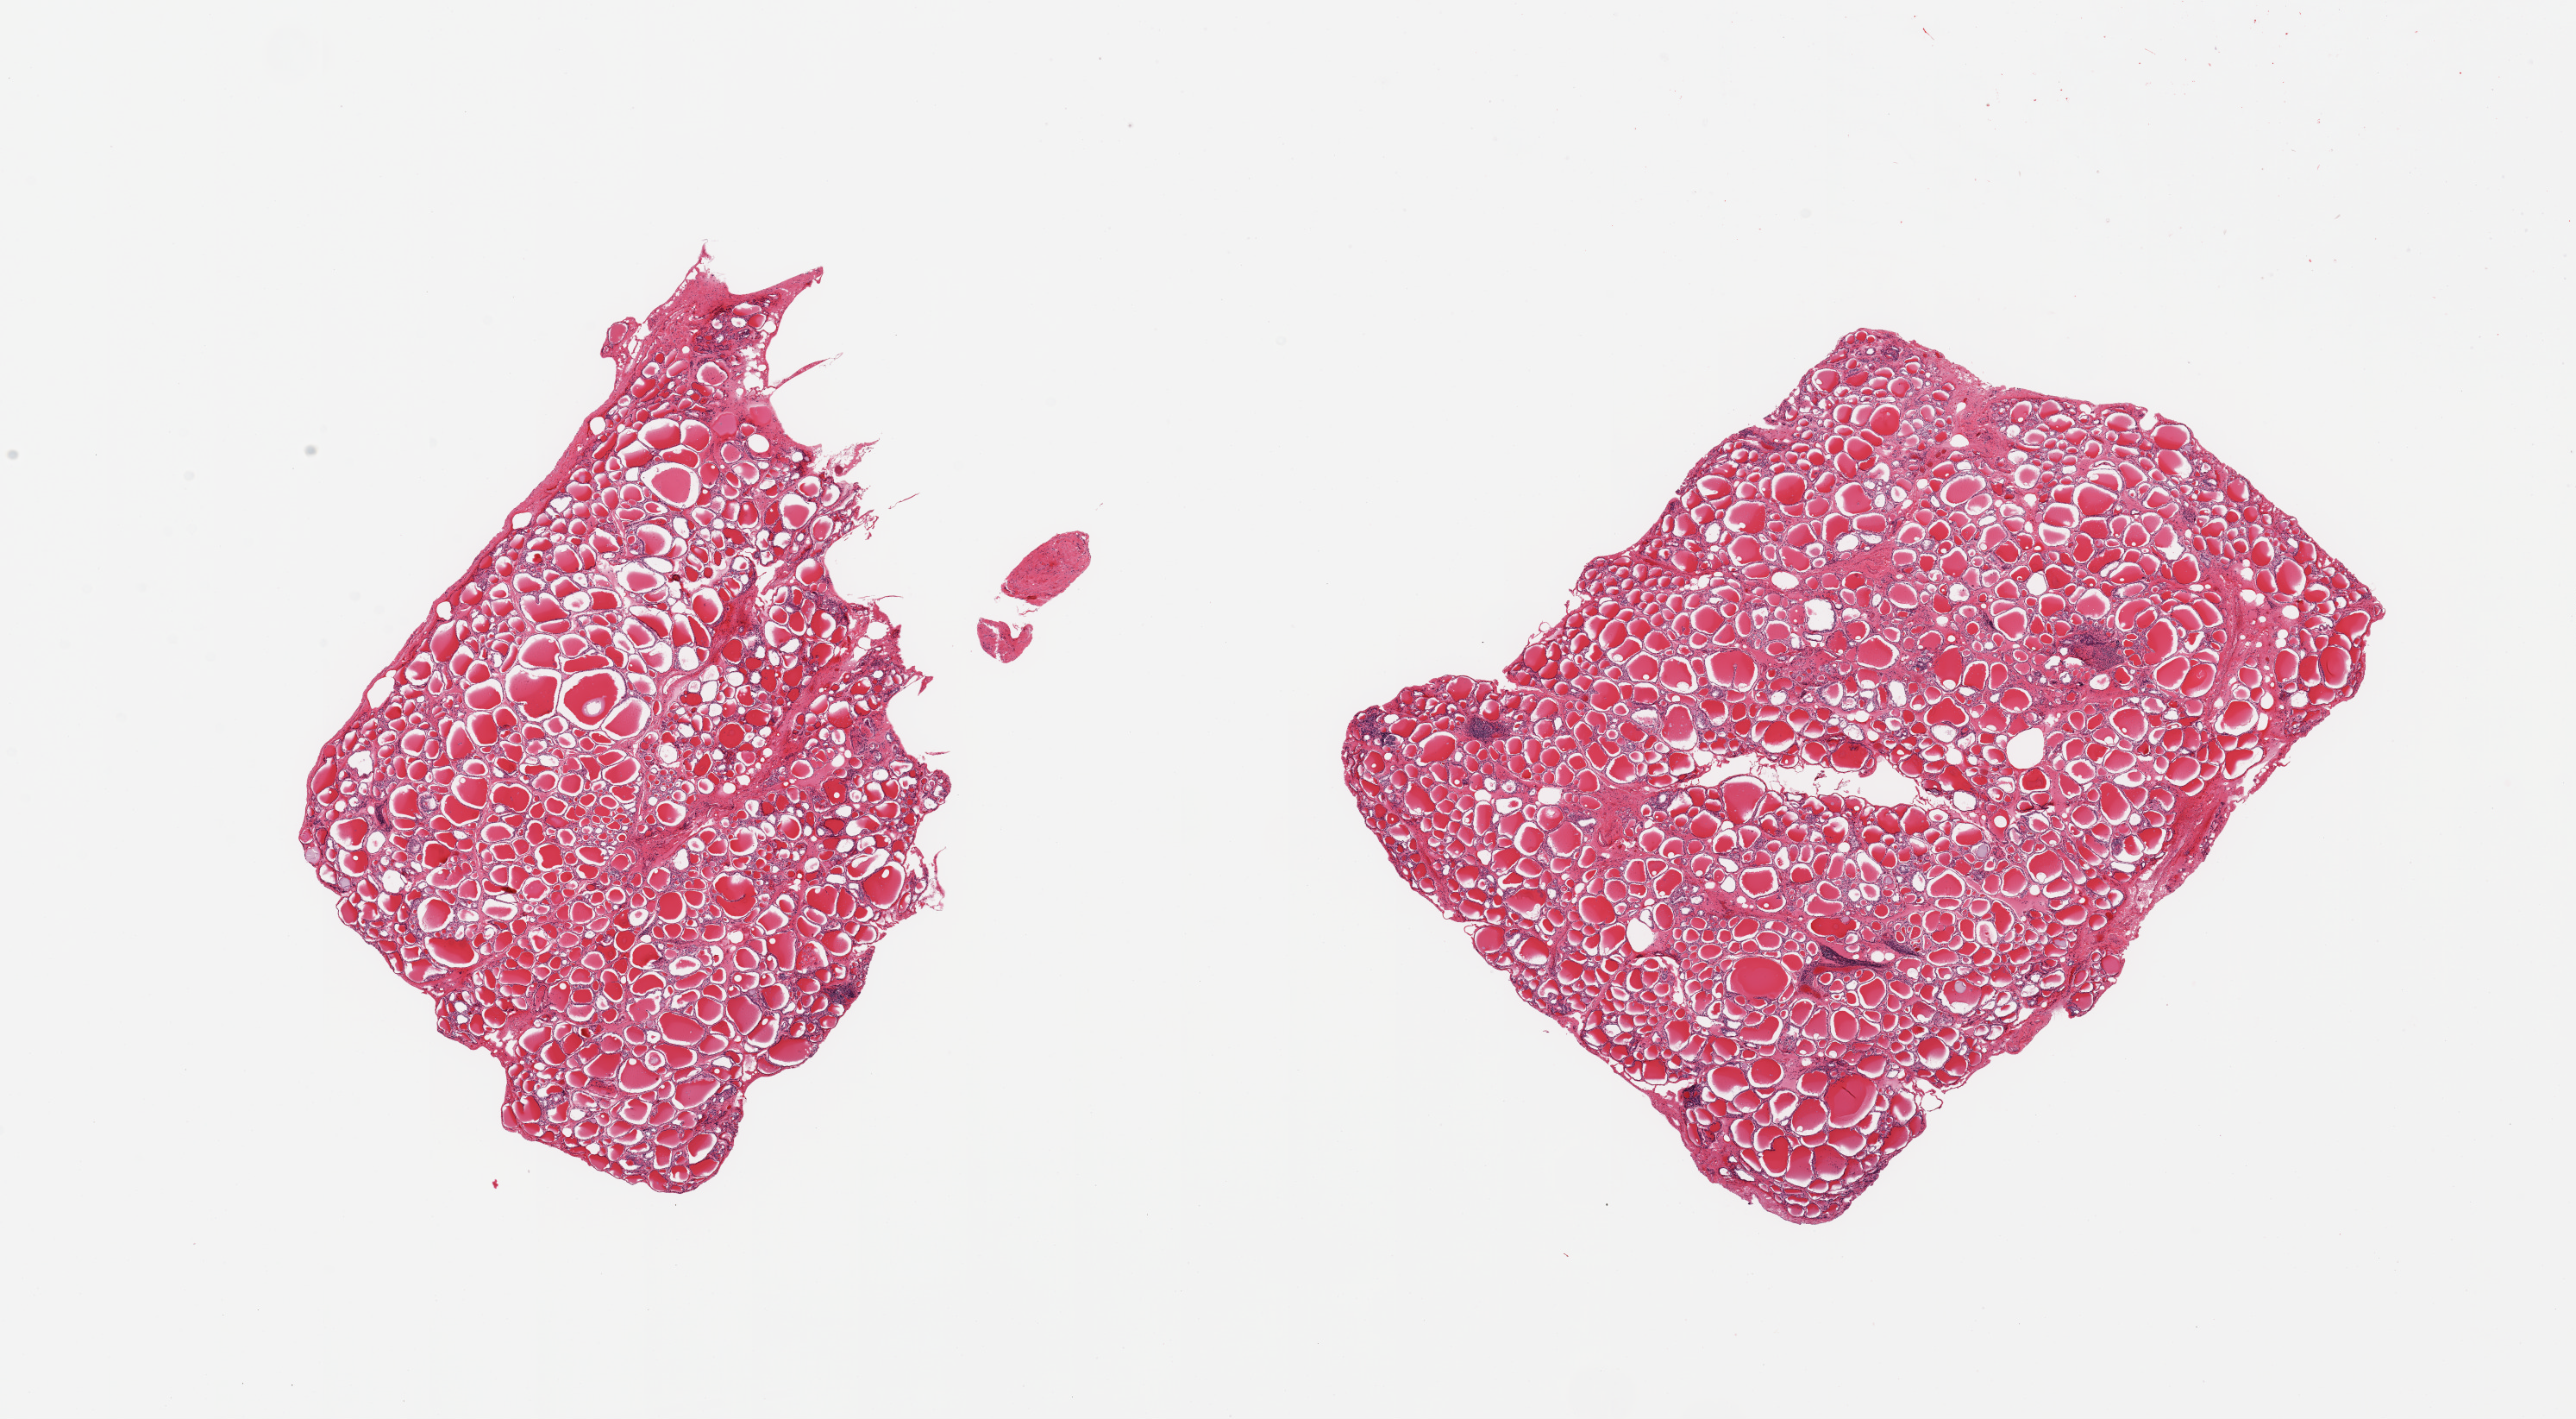
Digitized haematoxylin and eosin-stained section — shown as a low-resolution overview of the whole scanned area (about 23.6 x 13.0 mm). PAXgene-fixed paraffin-embedded (PFPE) section. Sampled site (target tissue): thyroid. Donor tissue sample.
Review note (as recorded): 2 pieces, no abnormalities.